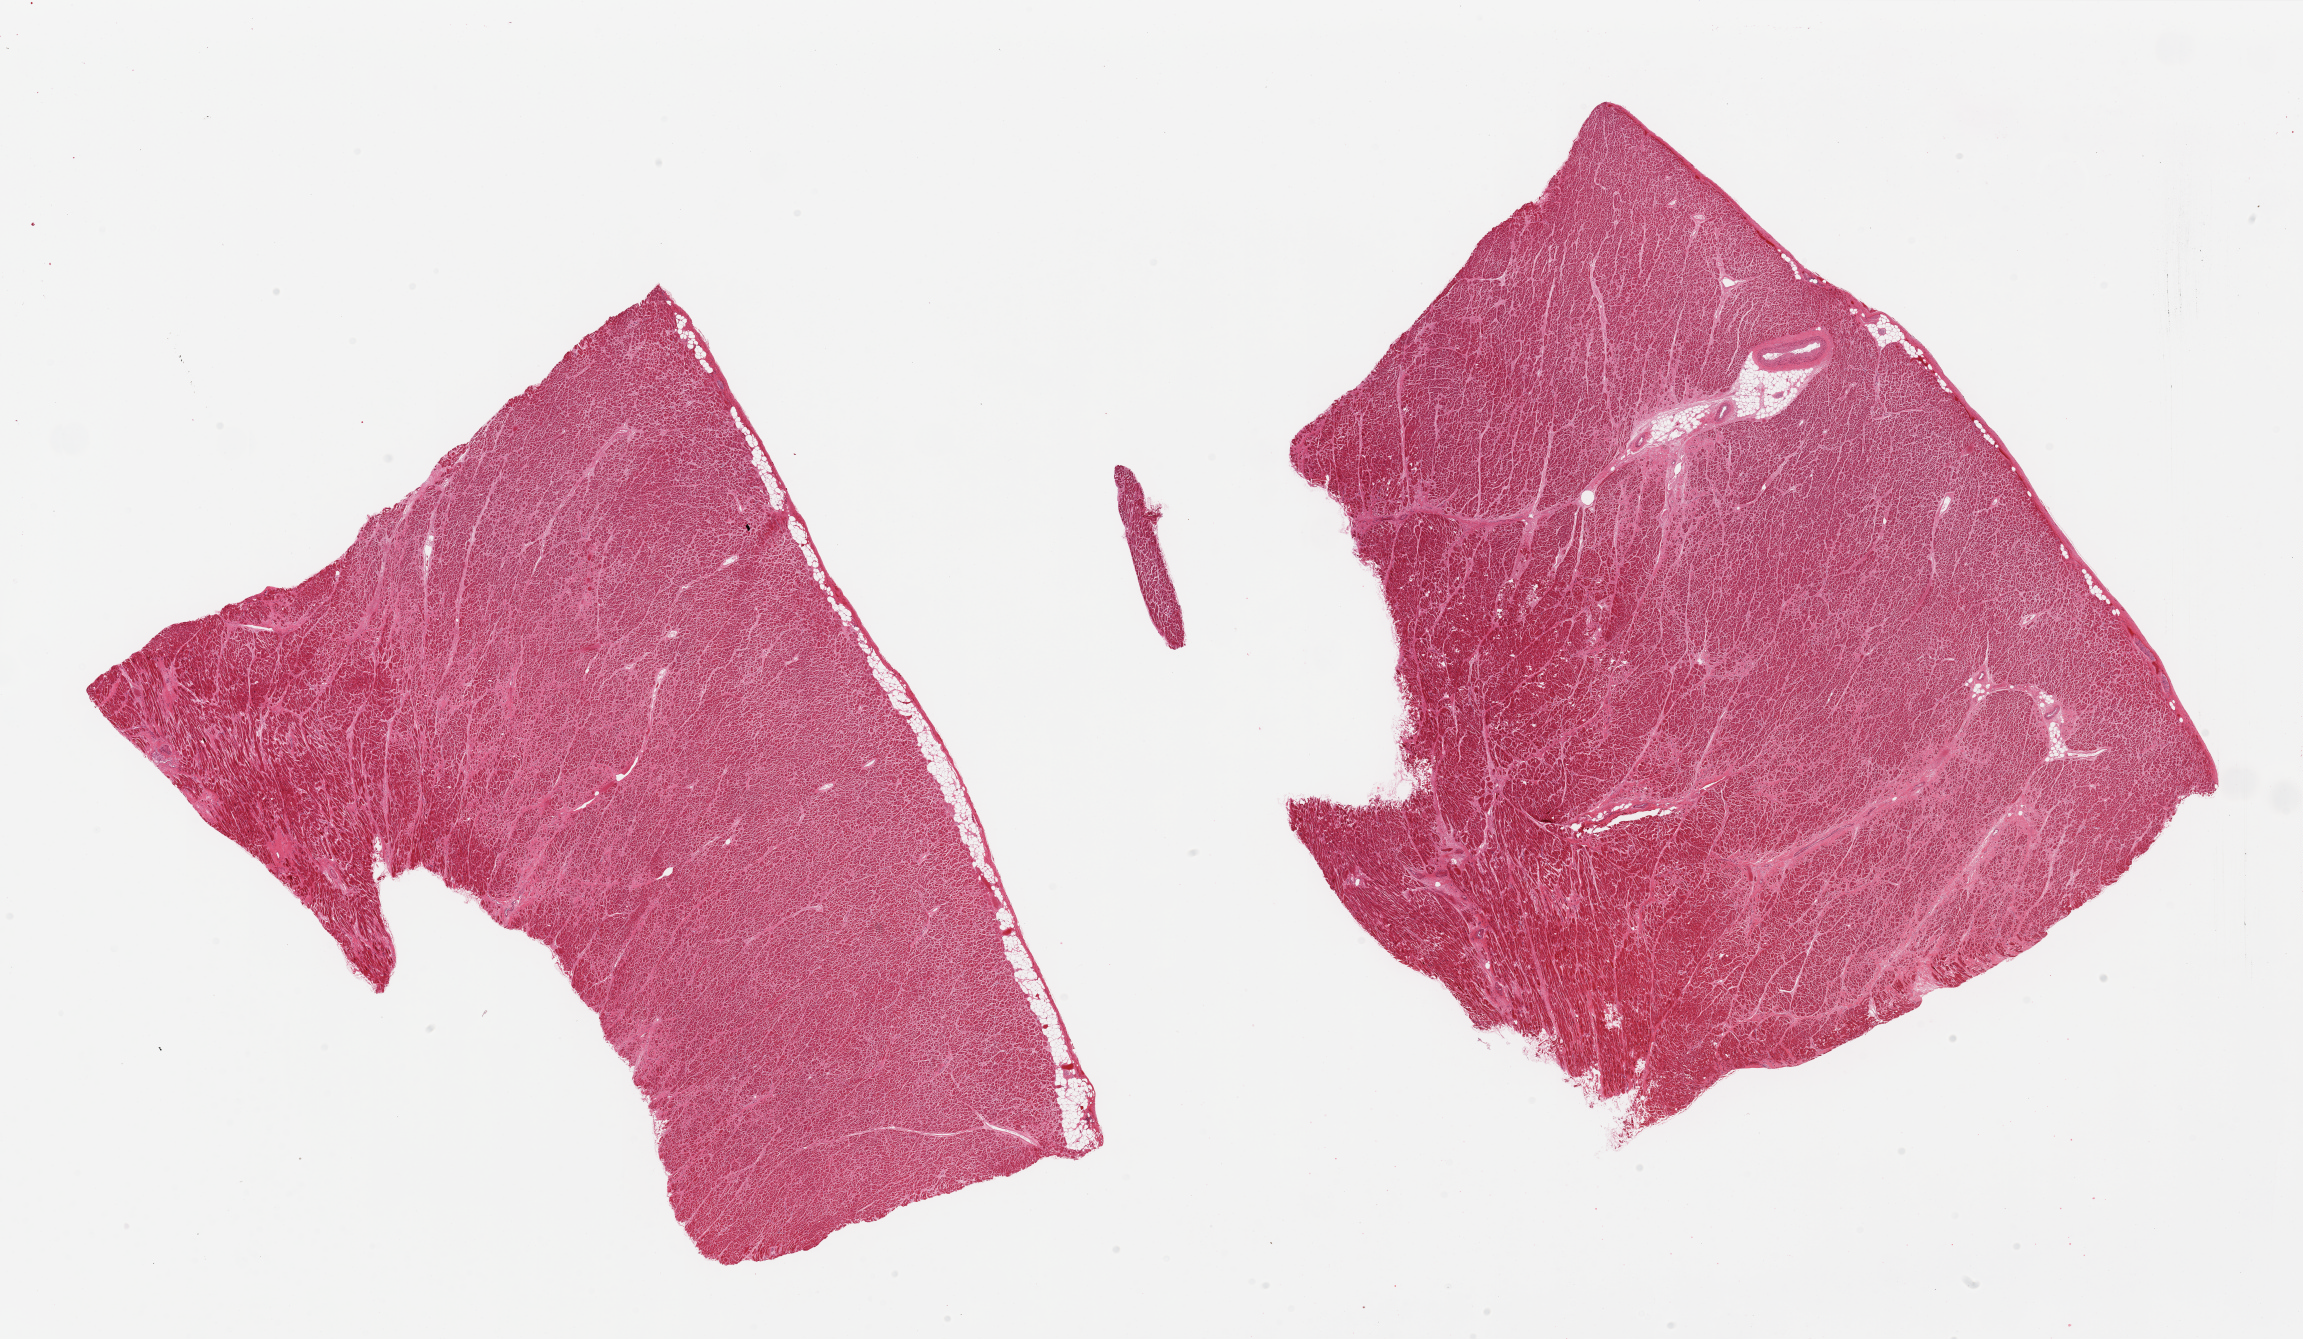
Whole-slide image, hematoxylin and eosin (H&E) stain — whole scanned area (about 36.4 x 21.2 mm, from a 20x scan) shown as a low-resolution overview, PAXgene-fixed paraffin-embedded (PFPE) section, target tissue: heart, donor tissue sample. Donor sex: male.
- pathologist's review note for this sample: 2 pieces; myocyte hypertrophy, interstitial and patchy fibrosis